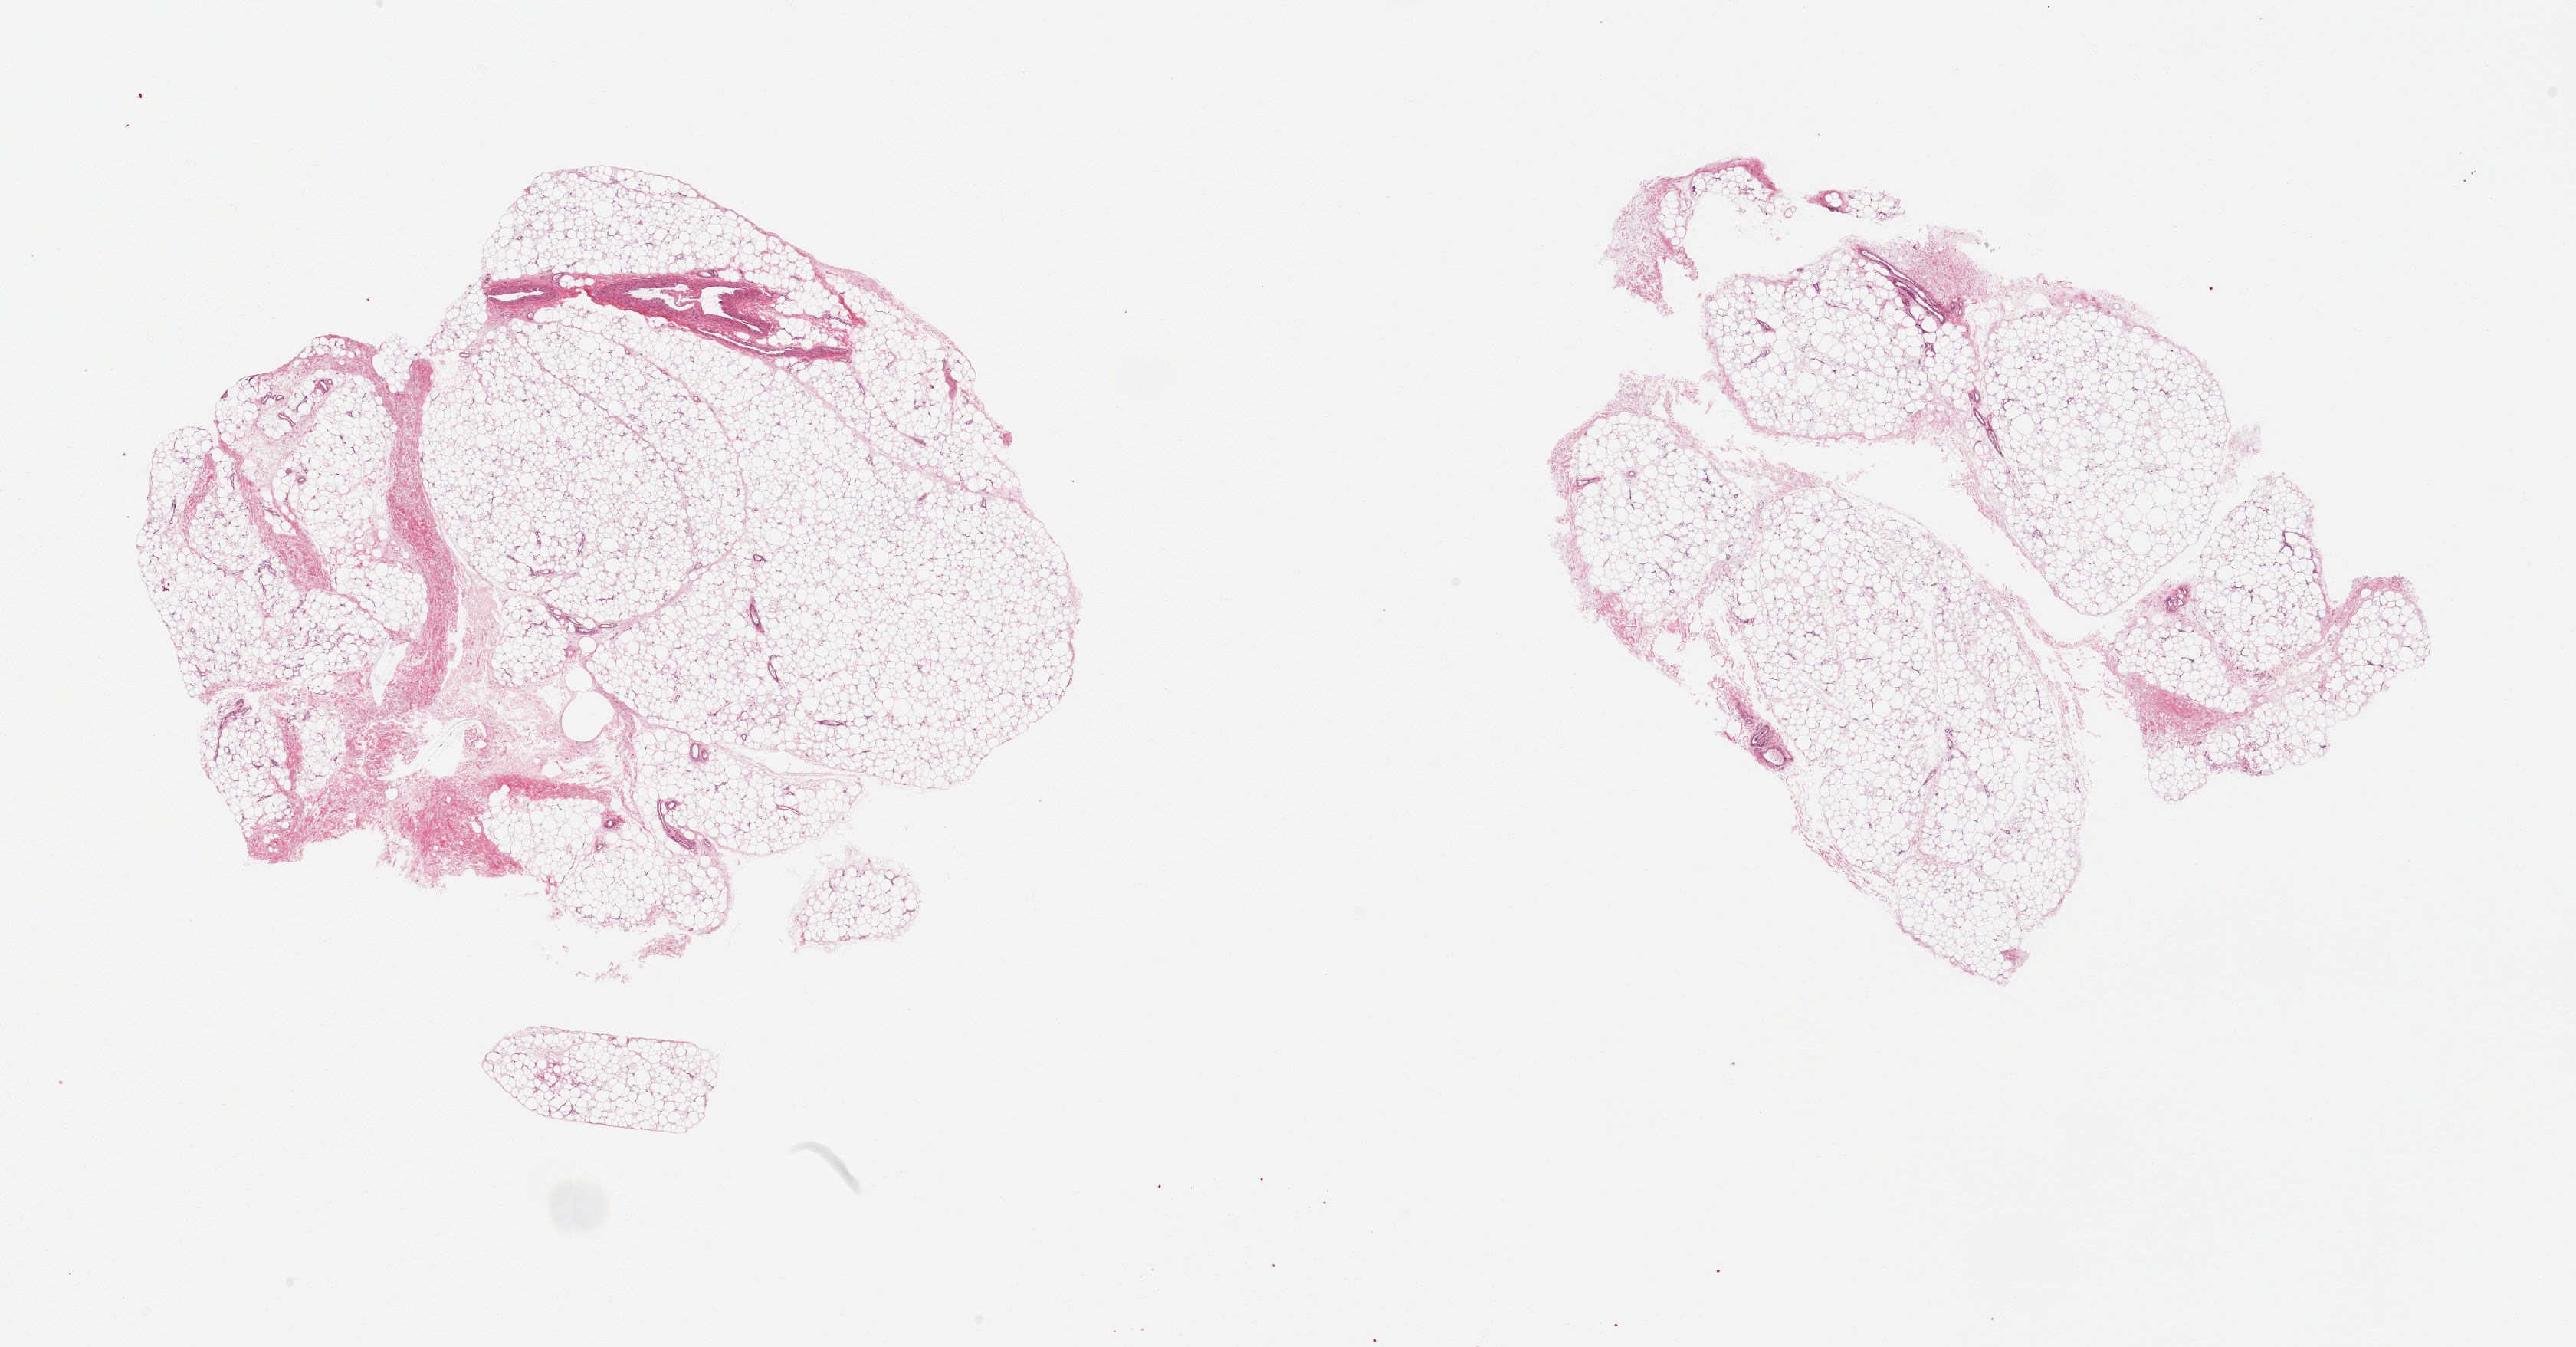
Haematoxylin and eosin whole-slide image, a low-resolution overview of the entire scanned area, about 26.6 x 13.9 mm. PAXgene-fixed, paraffin-embedded tissue. Sampled site (target tissue): adipose tissue. Donor tissue sample. Donor sex: male.
- review note (as recorded): 2 pieces, ~15-20% fascia/vascular elements